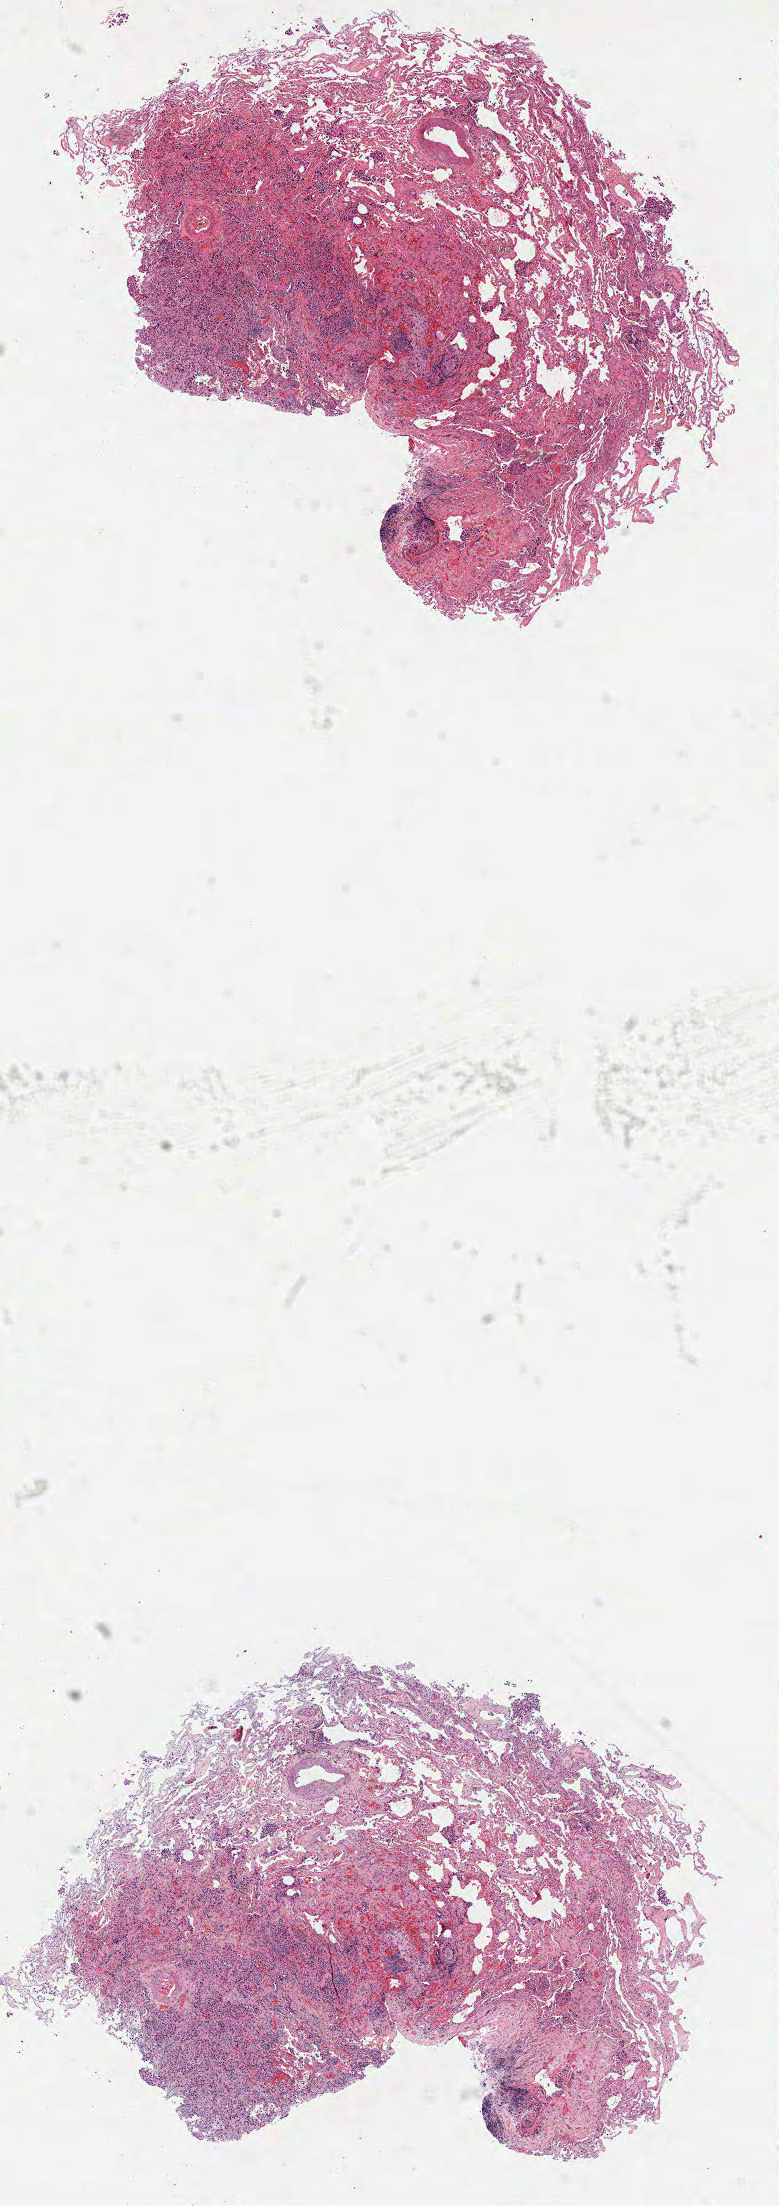
H&E-stained whole-slide image — shown as a low-resolution overview of the whole scanned area (about 6.3 x 17.8 mm, from a 40x scan); formalin-fixed paraffin-embedded (FFPE) diagnostic section; sample: primary tumour, lung. Female, age 65 years at initial diagnosis.
Diagnosis: Adenocarcinoma, NOS (lower lobe, lung).